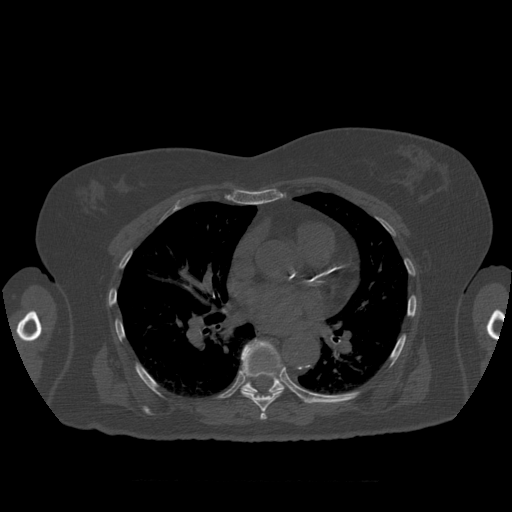
CT including the spine, one axial slice; slice 390 of 399 in the series (ordered by position); 120 kVp; bone window (W 1800 / L 400 HU); 1.25 mm slice thickness; 512 × 512 image matrix, field of view 404 × 404 mm. Patient age 81 years. Case-level facts recorded for this patient, not image findings: primary cancer: renal; vertebrae with lytic lesions (as recorded): L1.
Annotated regions visible in this slice (semi-automatic segmentation, software-assisted and operator-edited):
- T7 vertebra: bounding box <241,339,284,420> (left, top, right, bottom; pixels)
- T8 vertebra: <241,341,285,394>